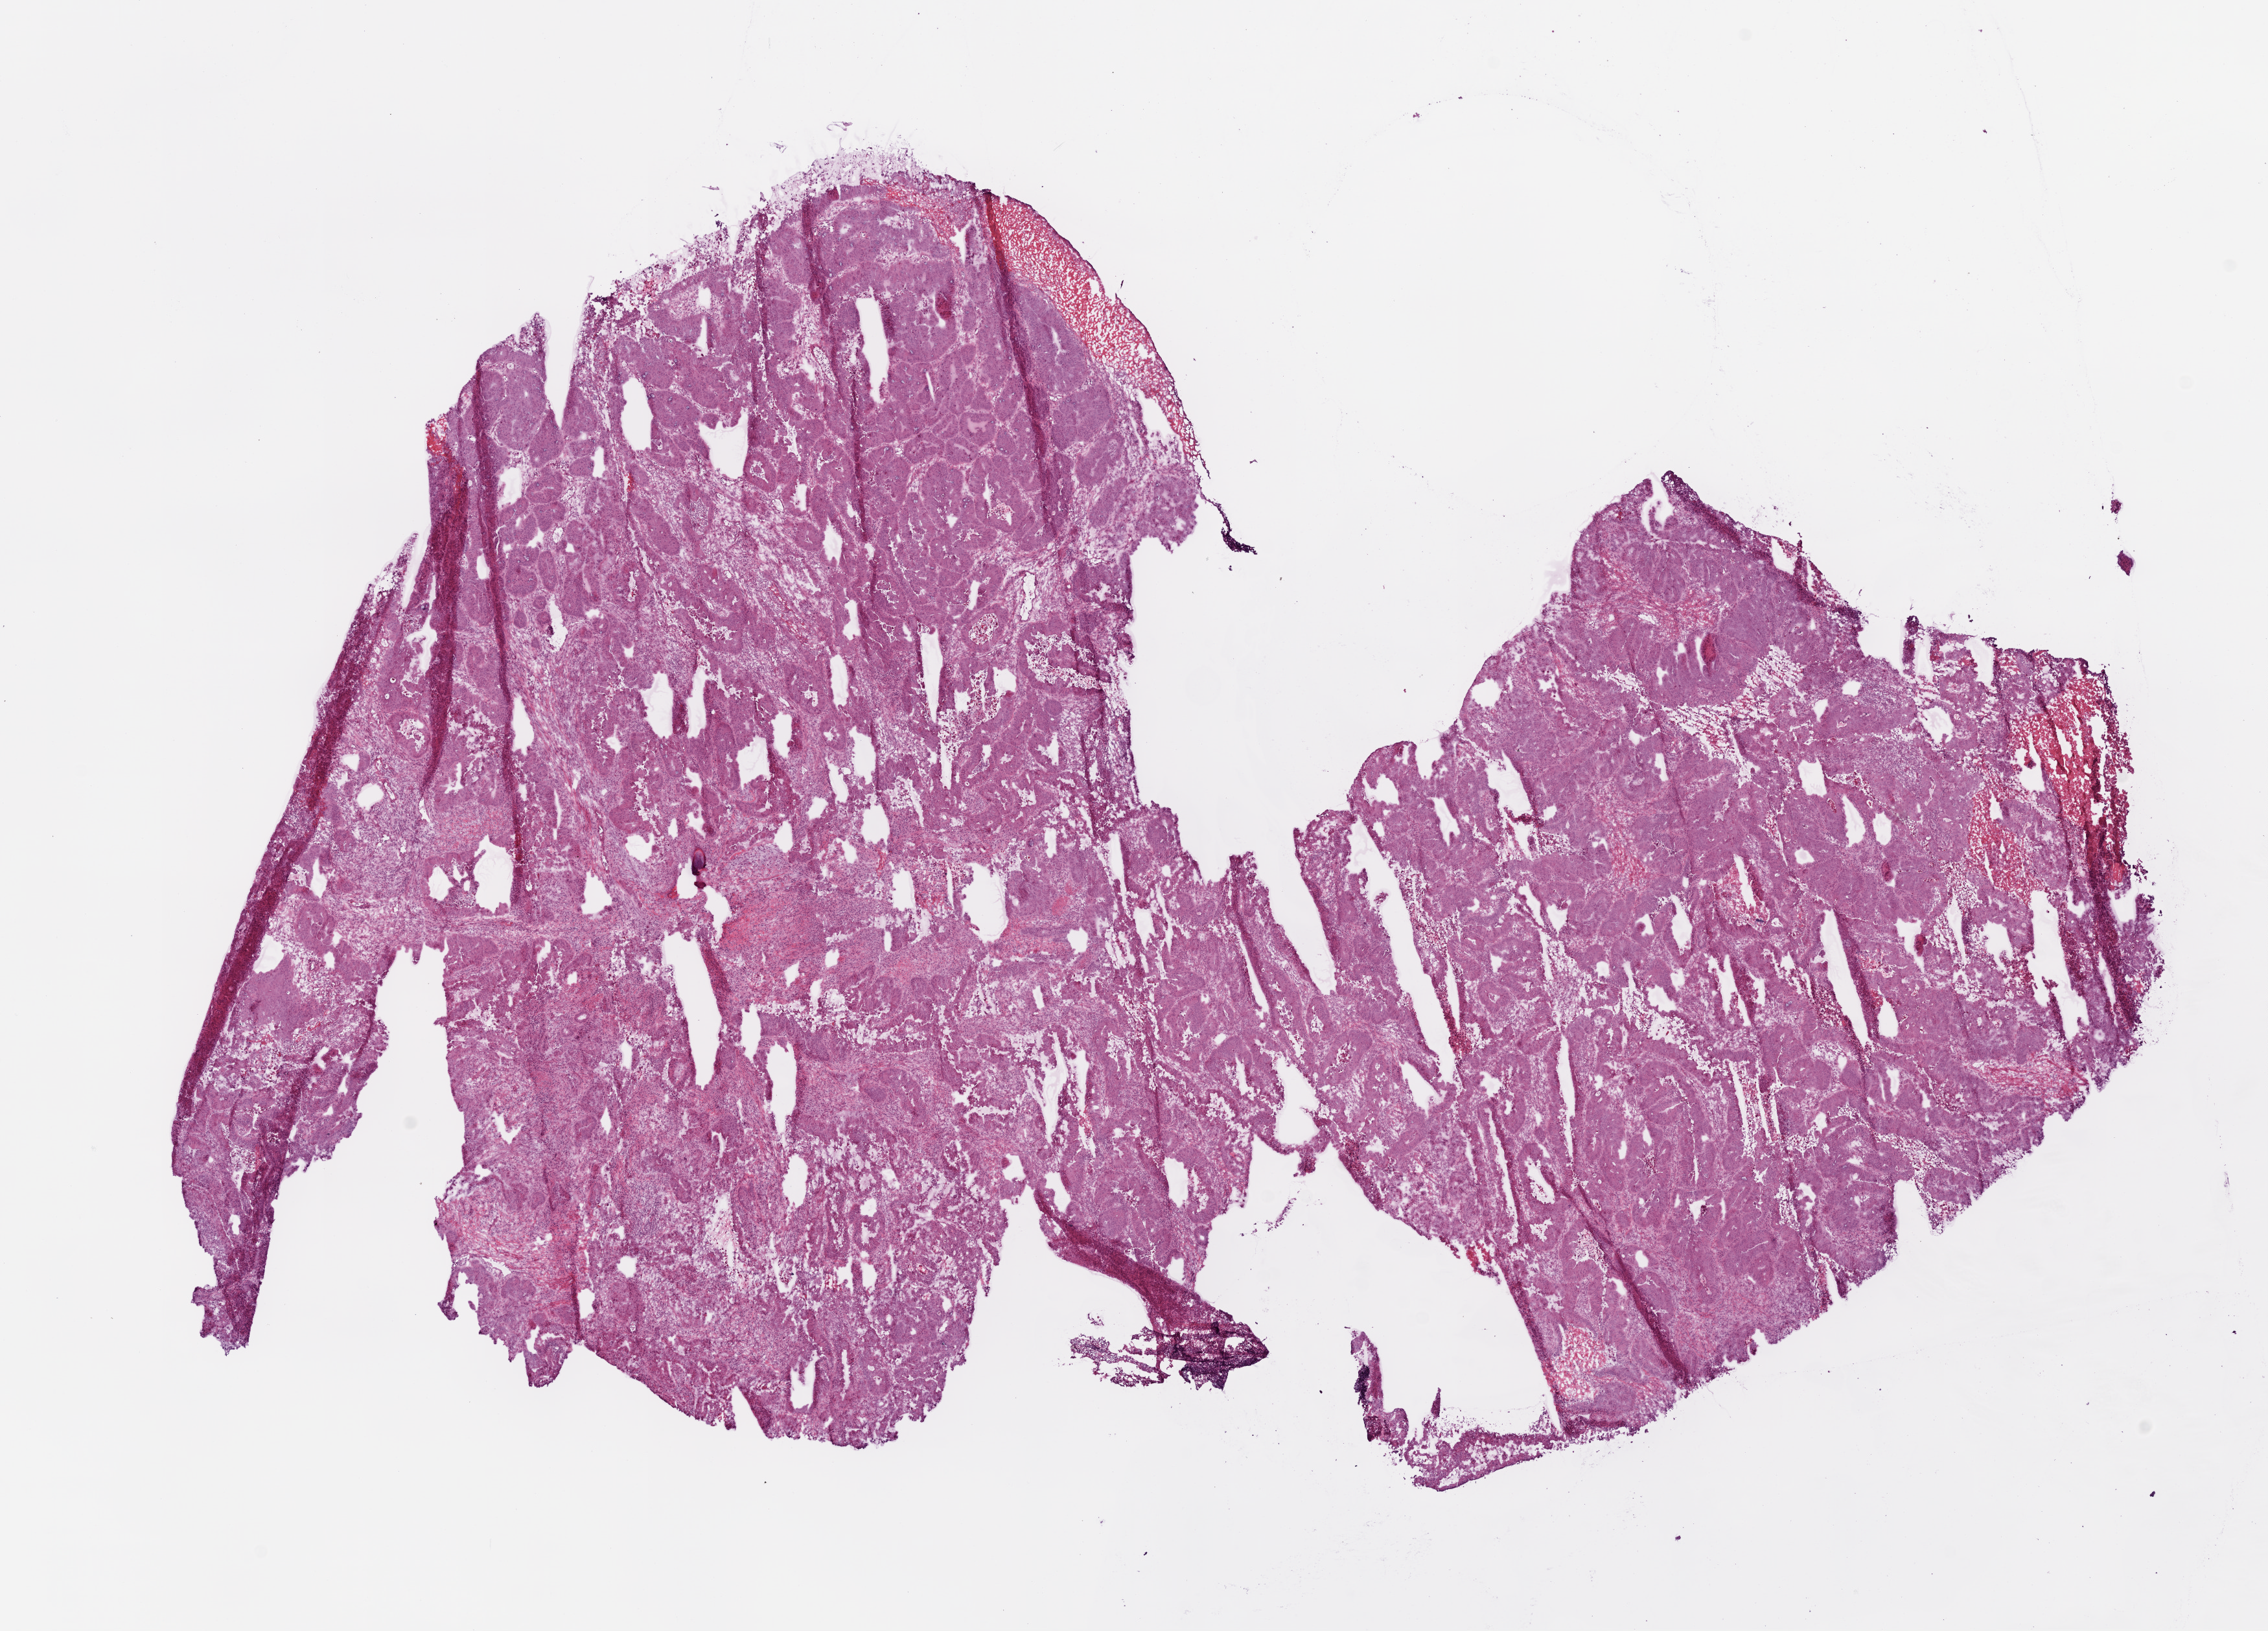
H&E whole-slide image — low-resolution overview of the scanned area, about 14.0 x 10.1 mm (acquisition: 20x scan), frozen section, sample: primary tumour, colon. Male, age 76 years at initial diagnosis.
Pathologic diagnosis: Adenocarcinoma, NOS (cecum).